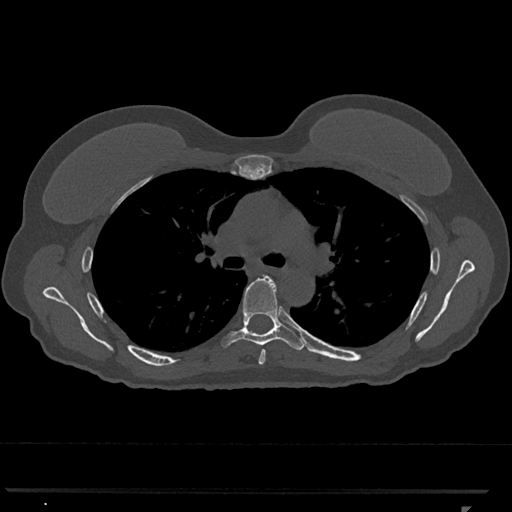
CT including the spine, one axial slice. Position 769 of 793 along the scan axis. Reconstruction kernel Br40s/3. Bone window (W 1800 / L 400 HU). 512 × 512 image matrix, field of view 380 × 380 mm. Patient: female, 62 years. From the clinical record (not read from this slice): primary cancer: renal.
Structures marked on this image (semi-automatically segmented with operator editing):
- T5 vertebra: bounding box (x1, y1, x2, y2) in pixels: (258, 349, 266, 365)
- T6 vertebra: (222, 276, 305, 350)